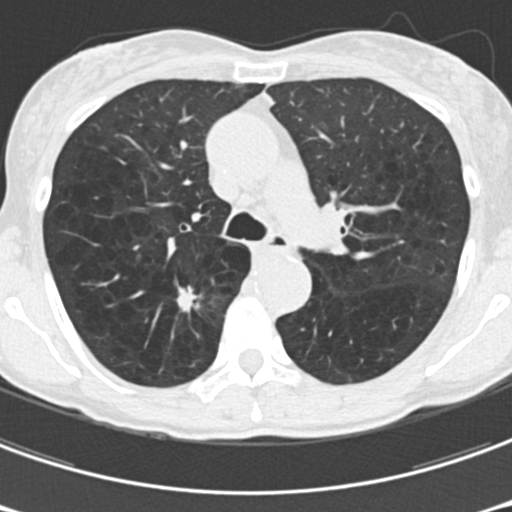
Low-dose screening chest CT, one axial slice; position 115 of 176 along the scan axis; reconstruction kernel B30f; lung window (W 1500 / L -600 HU); 512 × 512 image matrix, field of view 277 × 277 mm.
Structures marked on this image (expert manual segmentation):
- lesion 1 (tumor, upper lobe of right lung): bounding box (x1, y1, x2, y2) in pixels: (177, 286, 199, 312)